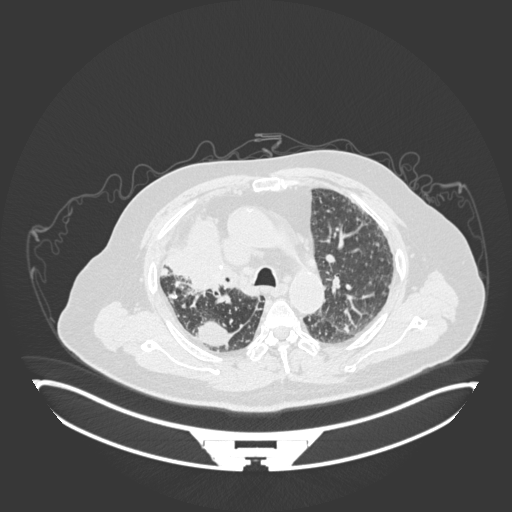
Chest CT, one axial slice; slice 125 of 201 in the series (ordered by position); 120 kVp; lung window (W 1500 / L -600 HU); 1 mm slice thickness; 512 × 512 image matrix, field of view 500 × 500 mm. Patient: male, 69 years. From the clinical record (not read from this slice): clinical TNM (as recorded): T4 N3 M1.
Annotated regions visible in this slice (rectangle marked by the reading radiologist):
- lung tumour (recorded histology: adenocarcinoma): bounding box <165,209,242,300> (left, top, right, bottom; pixels)